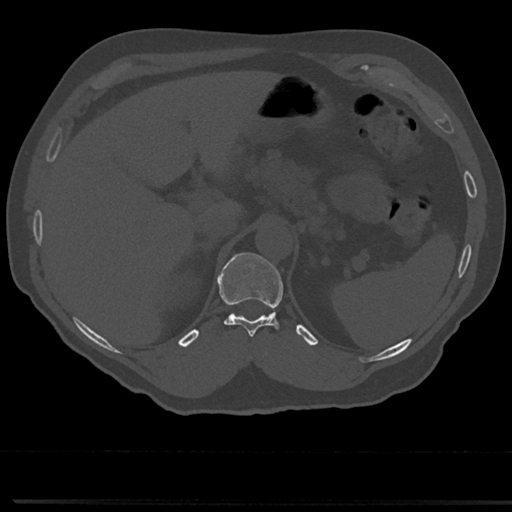
CT including the spine, one axial slice. Position 198 of 817 along the scan axis. Bone window (W 1800 / L 400 HU). 512 × 512 image matrix, field of view 355 × 355 mm. Male patient, age 61 years. Case-level facts recorded for this patient, not image findings: primary cancer: prostate.
Annotated regions visible in this slice (semi-automatic segmentation, software-assisted and operator-edited):
- T11 vertebra: box from (x=218, y=253) to (x=283, y=338) px